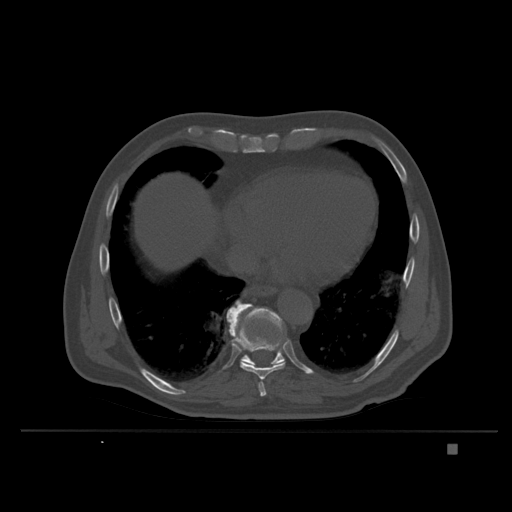
CT including the spine, one axial slice. Position 207 of 435 along the scan axis. Bone window (W 1800 / L 400 HU). 1.5 mm slice thickness. 512 × 512 image matrix, field of view 434 × 434 mm. Patient: male, 73 years. From the clinical record (not read from this slice): primary cancer: skin.
Outlined on this slice (semi-automatic segmentation, software-assisted and operator-edited):
- T10 vertebra: box from (x=240, y=304) to (x=285, y=365) px
- T9 vertebra: (x=226, y=300)–(x=288, y=397)